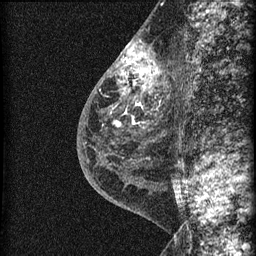
Breast MRI (dynamic contrast-enhanced), one sagittal slice. Position 28 of 60 along the scan axis. Dynamic contrast-enhanced series, image 2 of 3 at this slice position (ordered by acquisition). 1.5 T. TE 4.2 ms, TR 22.7 ms. 1.5 mm slice thickness. 256 × 256 image matrix, field of view 180 × 180 mm. Patient: female, 48 years. From the clinical record (not read from this slice): setting: breast cancer imaged before/during neoadjuvant chemotherapy; receptor status: triple-negative.
Outlined on this slice (semi-automatically segmented with operator editing):
- analysis volume of interest (the breast-tissue region the enhancement analysis was run in; not a lesion): bounding box [x1, y1, x2, y2] px = [115, 34, 169, 162]
- tumour enhancement mask (voxels above the 90 % enhancement threshold inside the analysis volume of interest): [121, 44, 159, 91]